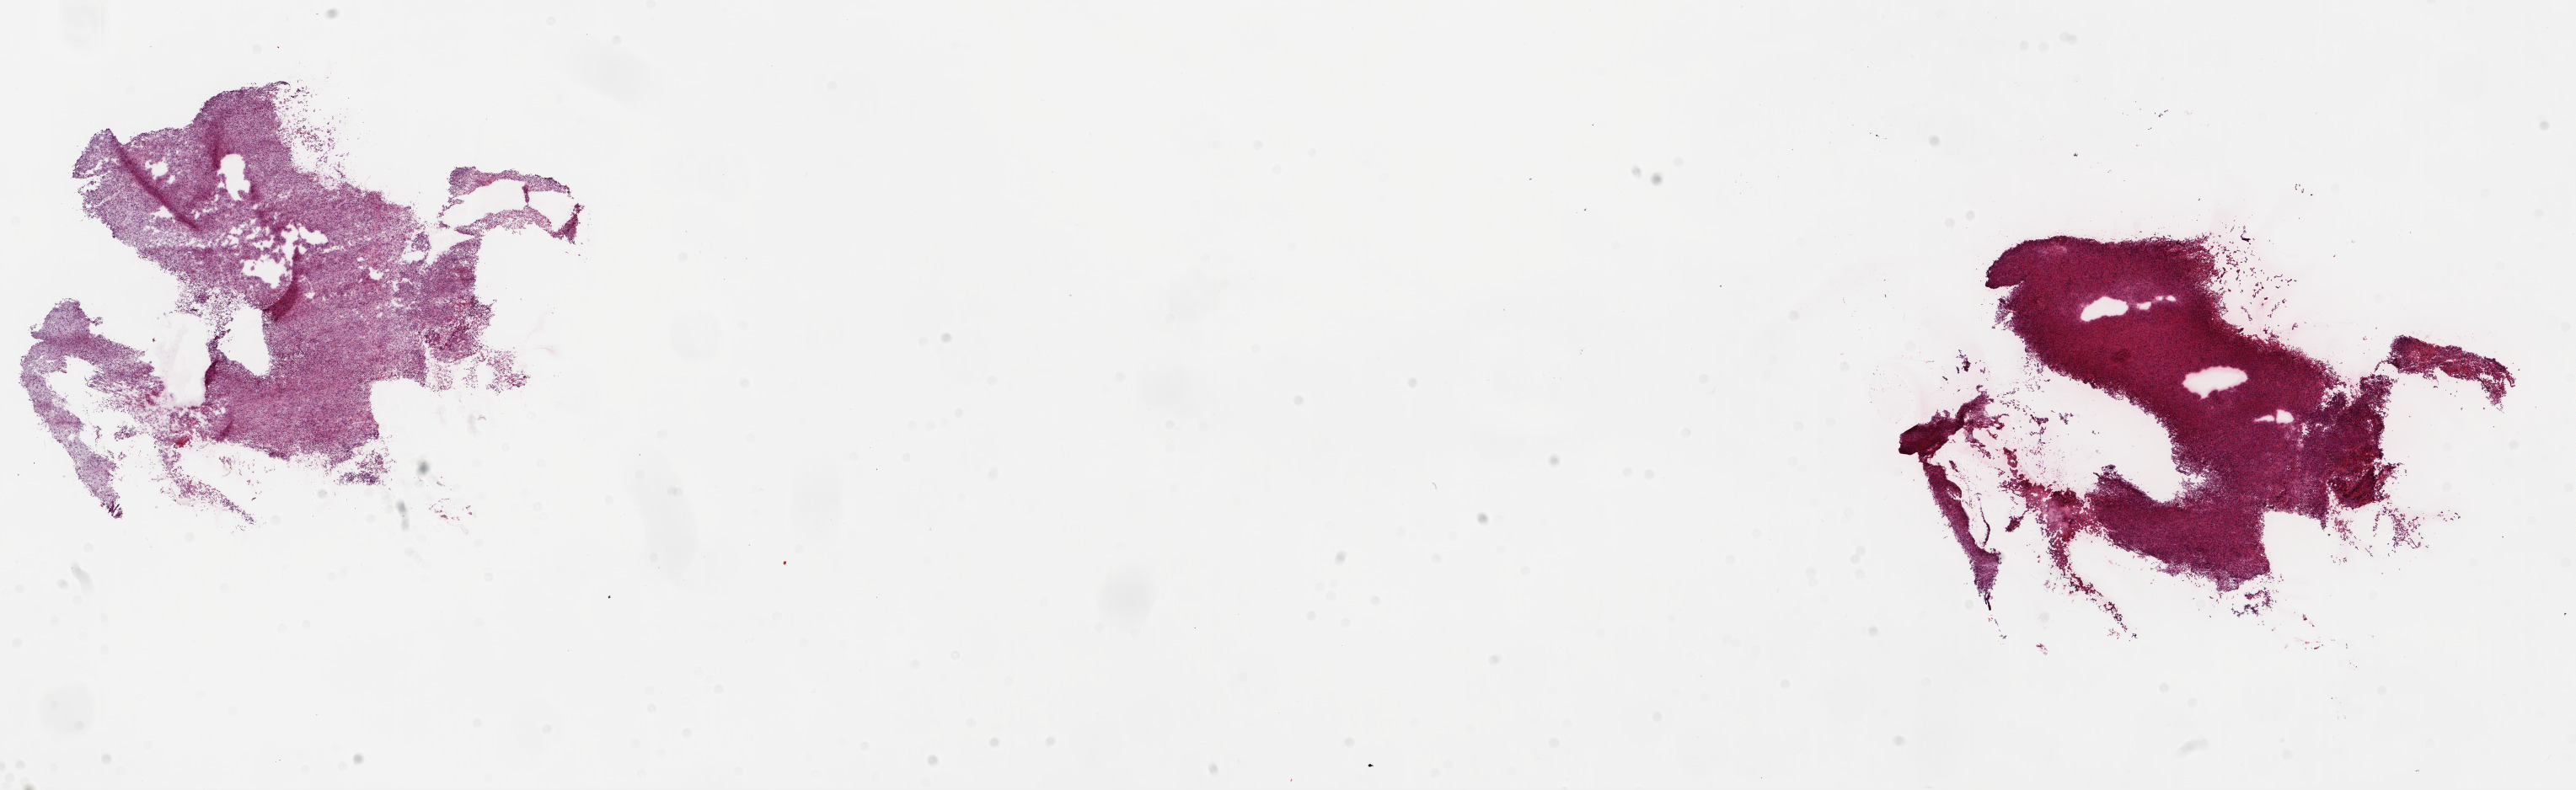
Digitized H&E tissue section (whole slide), whole scanned area (about 24.7 x 7.6 mm, from a 20x scan) shown as a low-resolution overview. Frozen section from the top of the tissue portion. Primary tumour sample from the brain. Male, age 69 years at initial diagnosis.
Diagnosis: Glioblastoma.